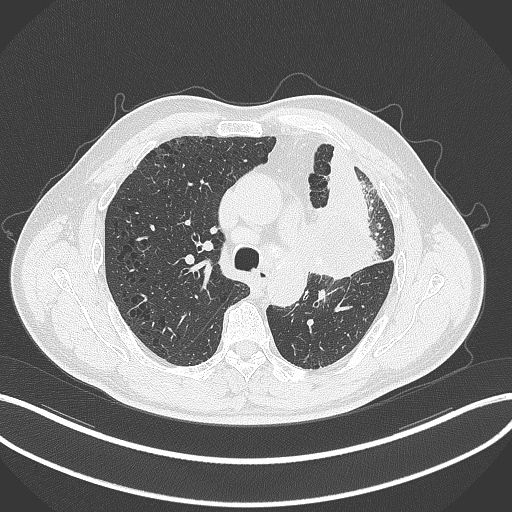
Chest CT, one axial slice; position 206 of 297 along the scan axis; 120 kVp; lung window (W 1500 / L -600 HU); 1 mm slice thickness; 512 × 512 image matrix, field of view 400 × 400 mm. Patient: male, 68 years. Case-level facts recorded for this patient, not image findings: clinical TNM (as recorded): T3 N3 M1.
Structures marked on this image (bounding box drawn by a radiologist):
- lung tumour (recorded histology: adenocarcinoma): bounding box [x1, y1, x2, y2] px = [305, 196, 385, 284]